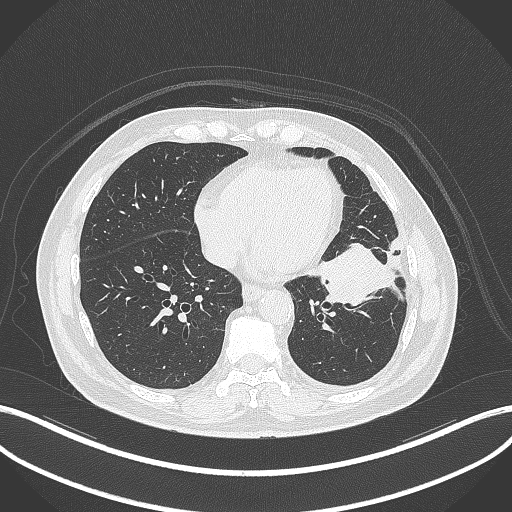
Chest CT, one axial slice. Slice 126 of 230 in the series (ordered by position). Reconstruction kernel B70f. Lung window (W 1500 / L -600 HU). 1 mm slice thickness. 512 × 512 image matrix. Male patient, age 68 years. Case-level facts recorded for this patient, not image findings: clinical TNM (as recorded): T2b N0 M0.
Outlined on this slice (rectangle marked by the reading radiologist):
- lung tumour (recorded histology: squamous cell carcinoma): bounding box <312,239,405,303> (left, top, right, bottom; pixels)